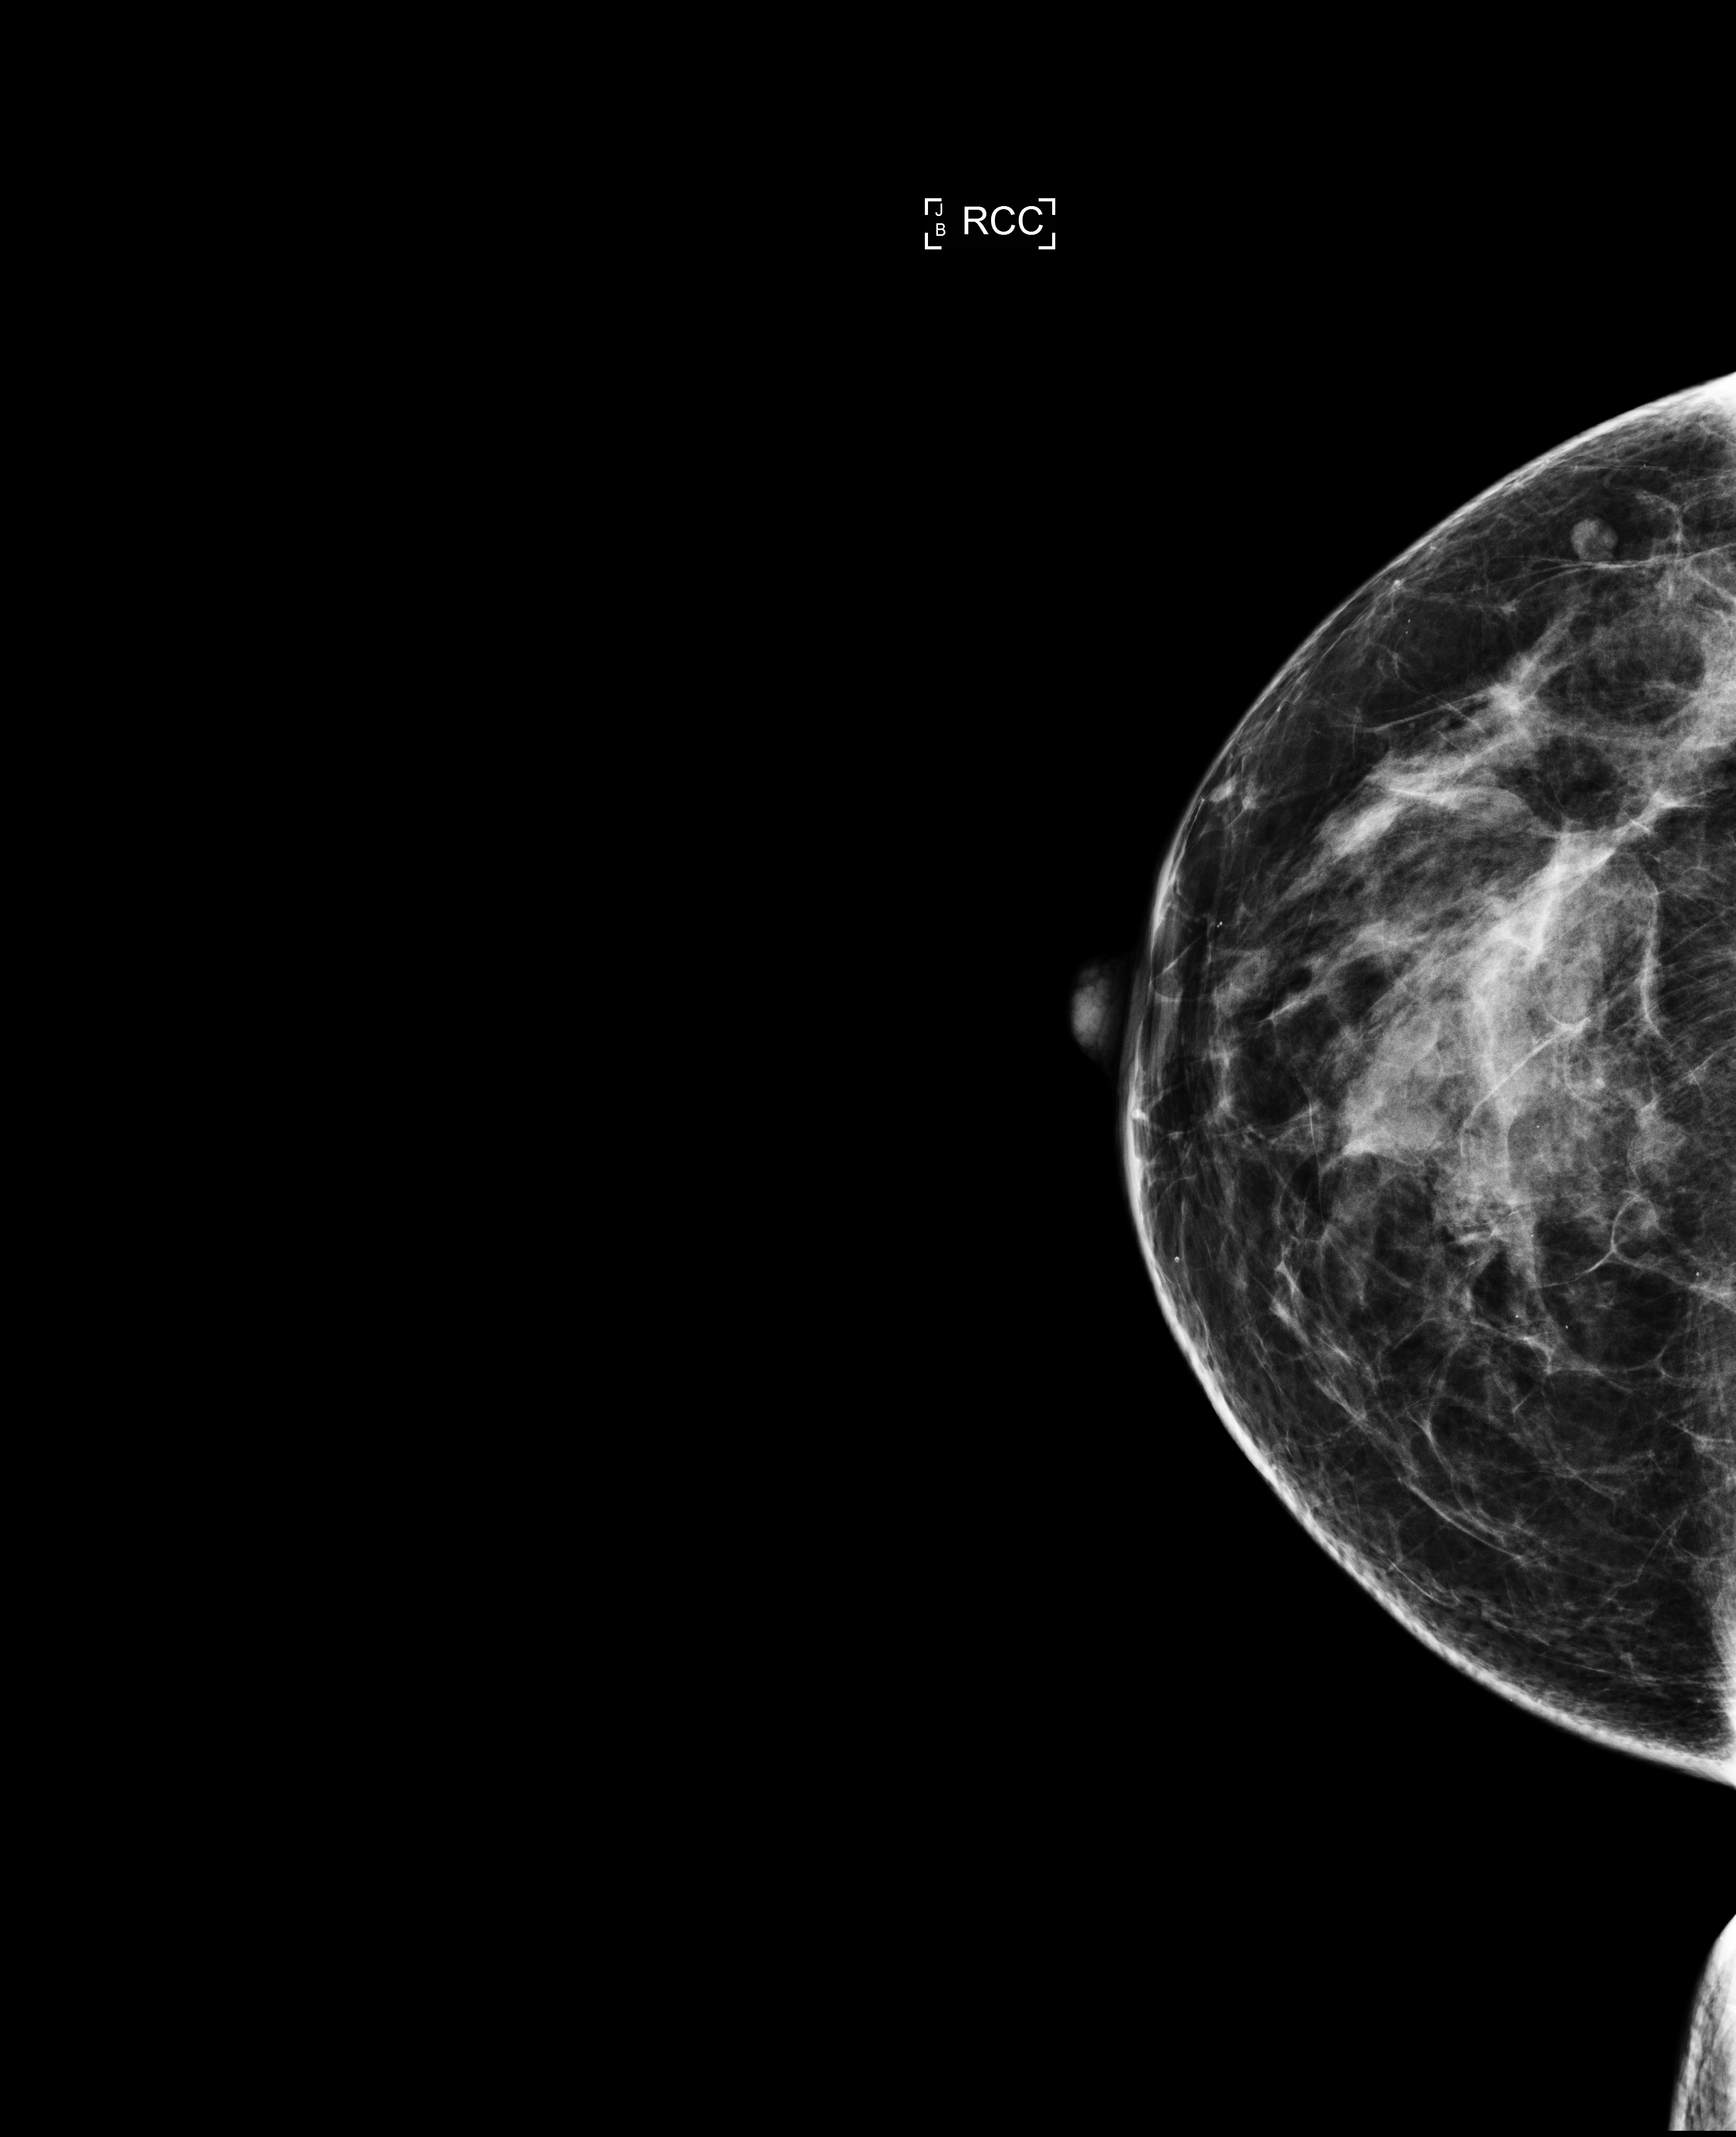
Digital mammogram (FFDM); right breast; craniocaudal (CC) view; annual screening mammography examination. Female patient, age 59 years.
Breast density at the screening exam (both breasts): heterogeneously dense (BI-RADS density category c). Final BI-RADS assessment for this screening round (tomosynthesis exam, both breasts): category 1. Recall: no recall after this screen.